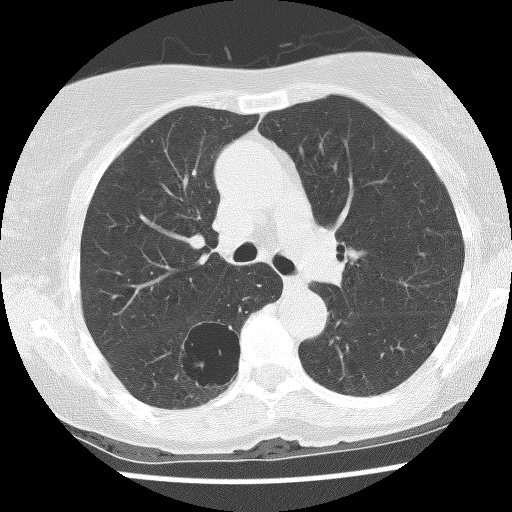
Low-dose screening chest CT, axial slice, first (baseline) screen, lung window (W 1500 / L -600 HU), 2.5 mm slice thickness, lung (sharp) reconstruction kernel (BONE), slice 47 of 136 in the series, 512 × 512 image matrix, field of view 300 × 300 mm. Female, age 69 years at enrolment. Former smoker at enrolment.
Lesion marked by an expert reader, box from (x=165, y=322) to (x=245, y=396) px. The screening reader recorded 2 non-calcified nodules or masses ≥4 mm on this exam (right lower lobe, right lower lobe); which of them this box marks is not recorded. Official screen result: positive, change unspecified: nodule(s) >= 4 mm or enlarging nodule(s), mass(es), or other non-specific abnormalities suspicious for lung cancer. Lung cancer was diagnosed 288 days after this screen: non-small cell carcinoma, right lower lobe, poorly differentiated (G3), stage IB (AJCC 6th edition), 36 mm at pathology.